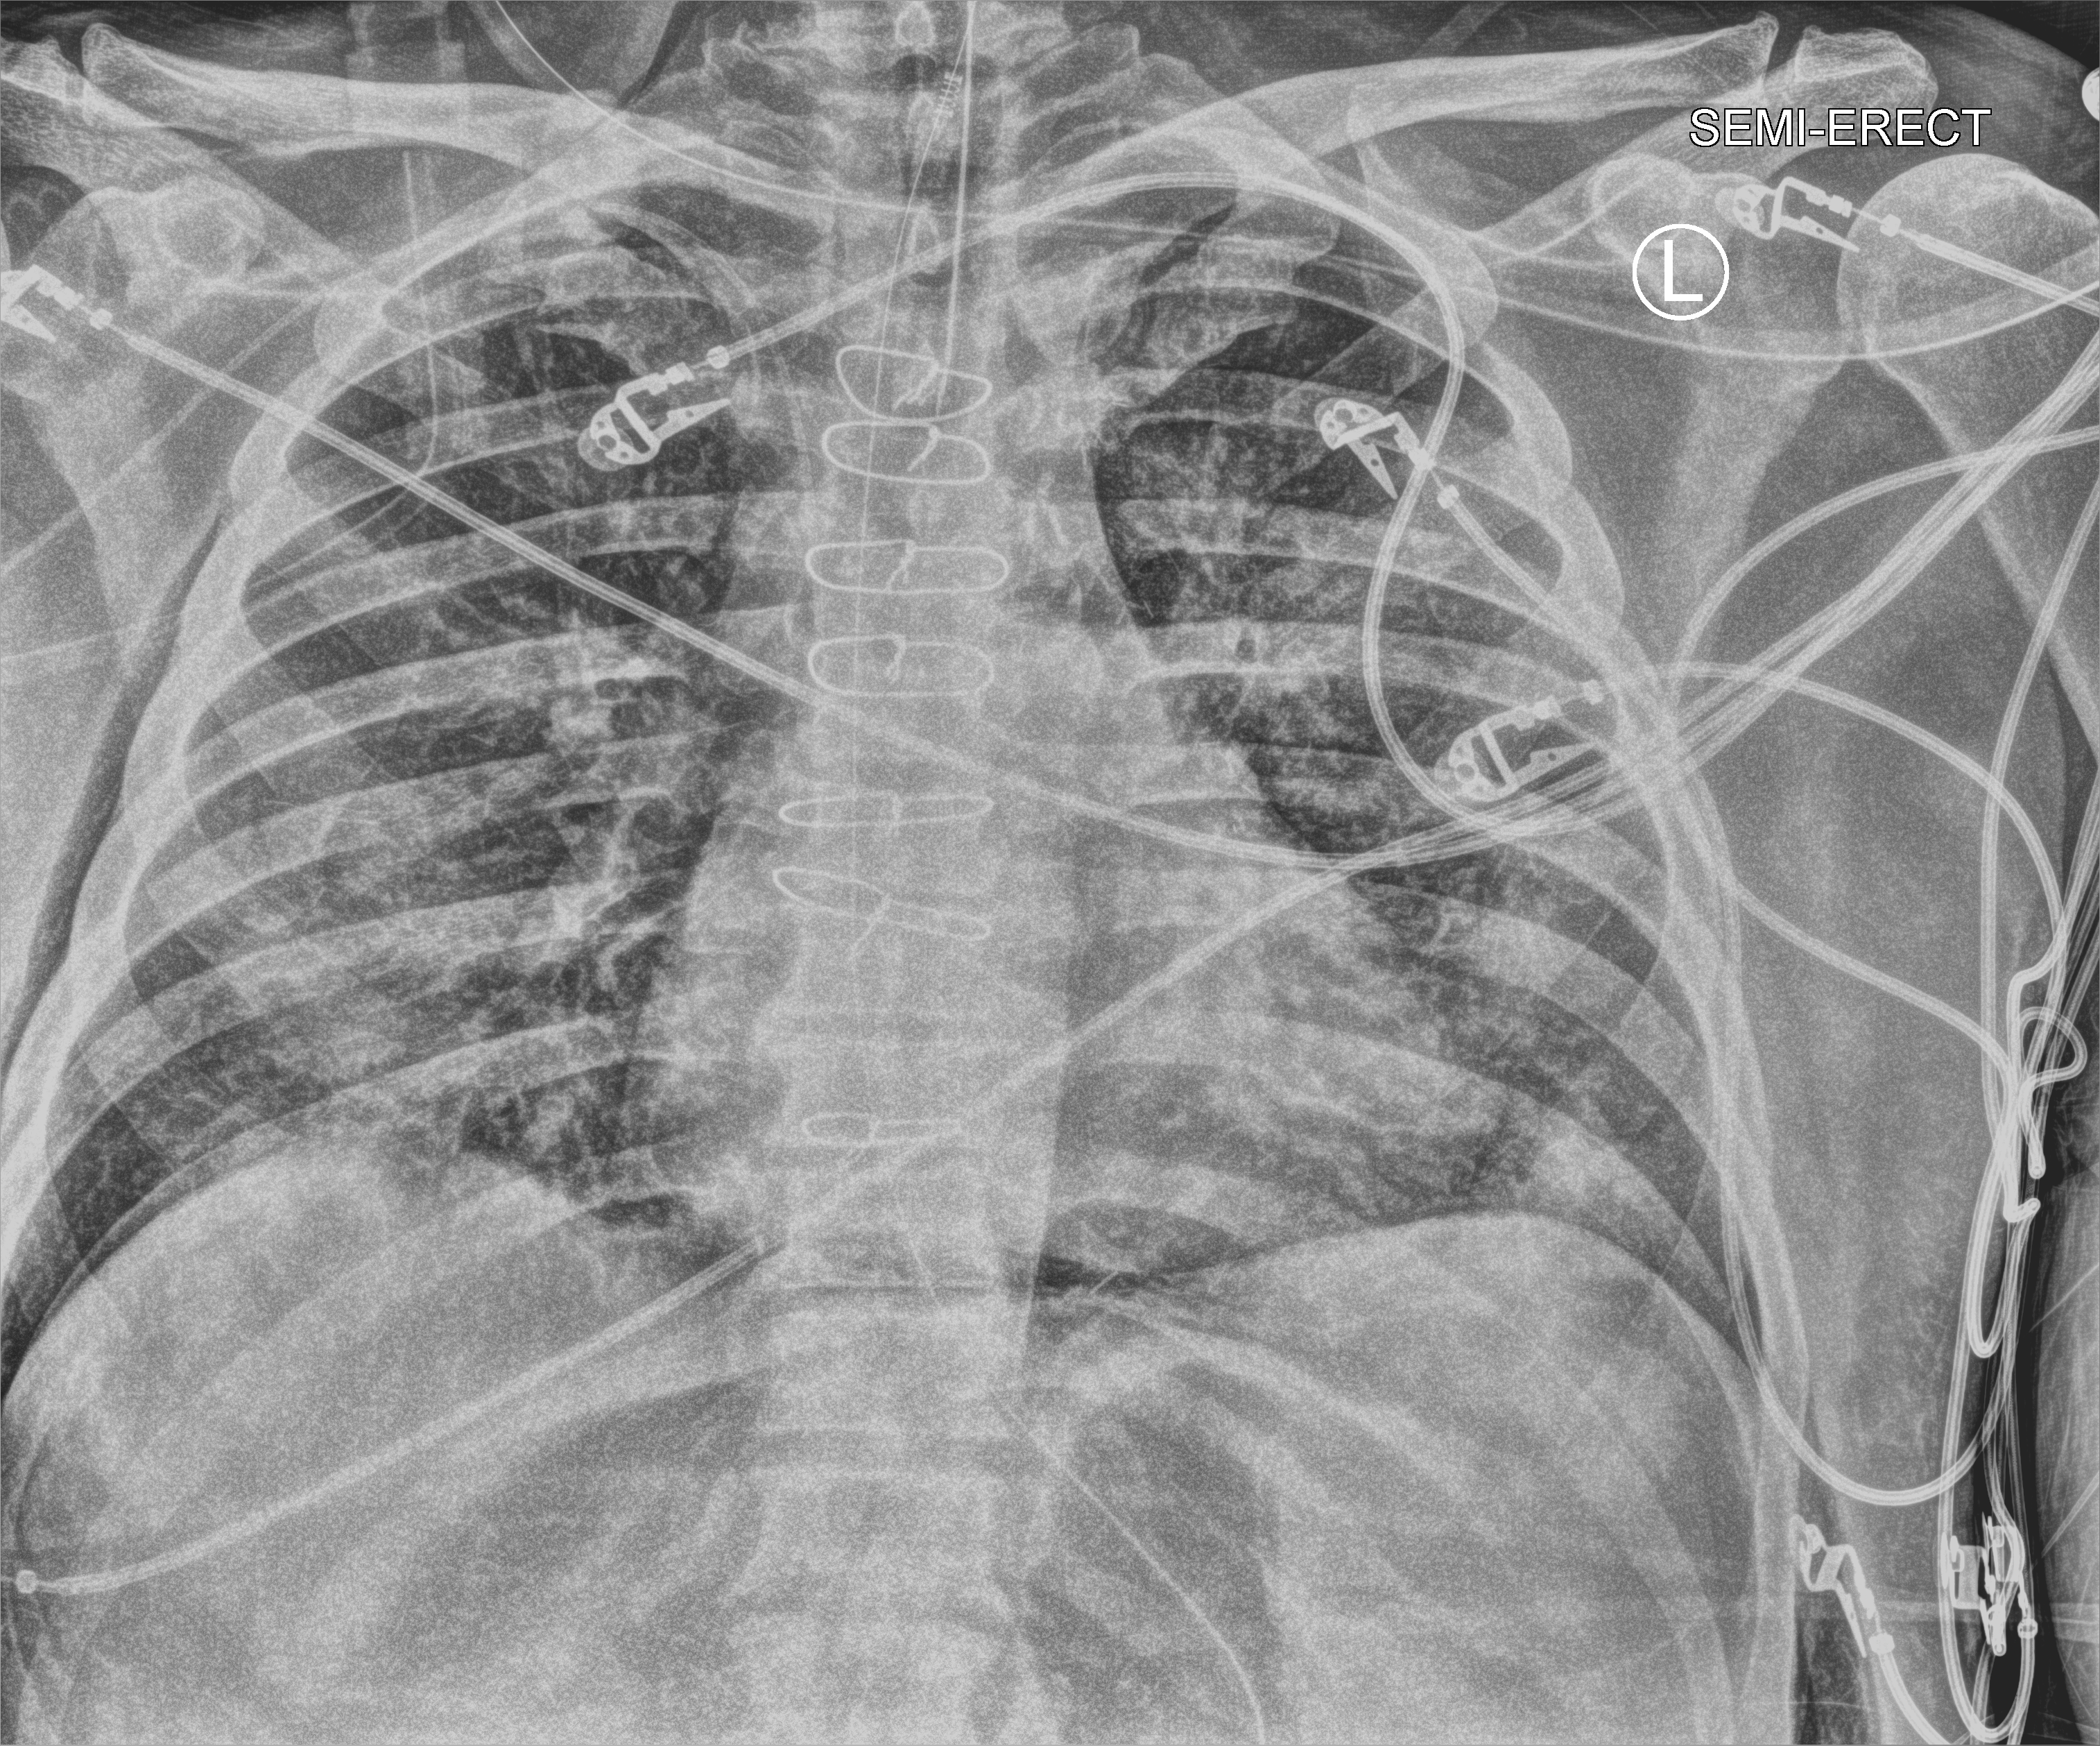
Bedside chest radiograph (computed radiography); anteroposterior (AP) projection. Patient hospitalised with COVID-19; male, aged 60–74 years.
Admission-level facts for this patient (not findings on this image; timing relative to this image not recorded):
- mechanically ventilated during this hospital stay: yes